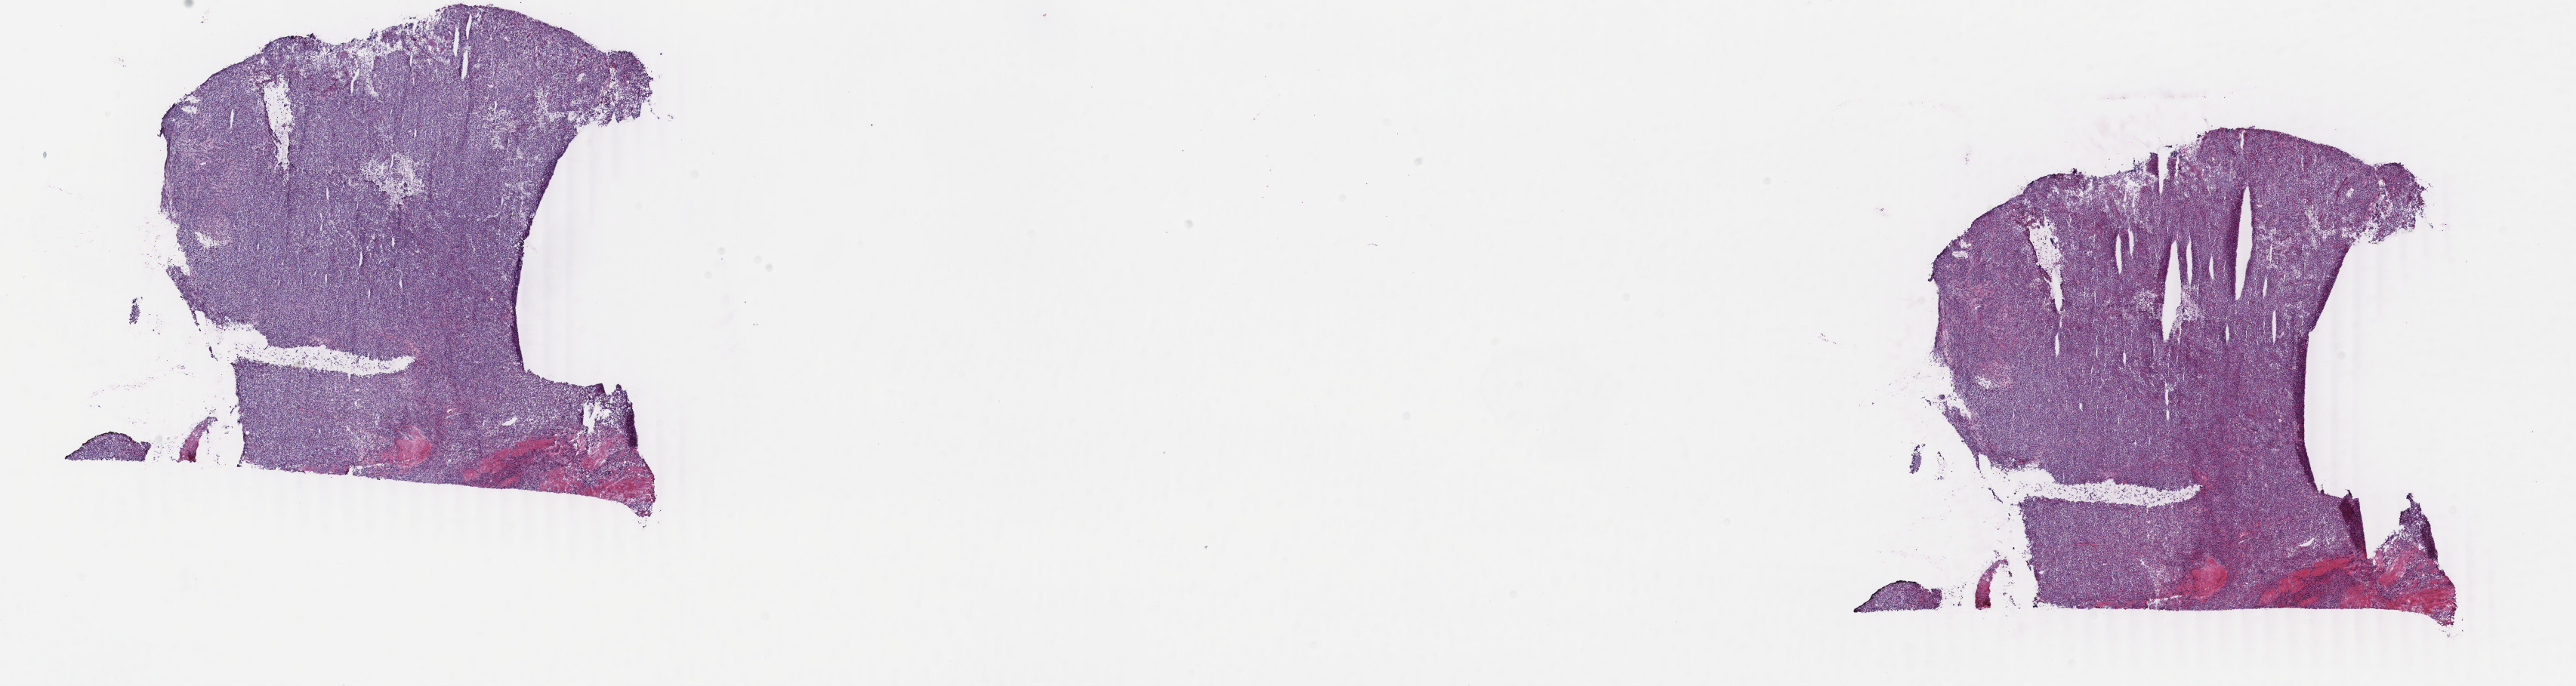
H&E-stained whole-slide image — whole scanned area (about 27.1 x 7.2 mm) shown as a low-resolution overview; frozen section; sample: primary tumour, bladder. Patient: female, age at initial diagnosis 57 years. Histologic grade: high grade. Composition of this section per pathologist review: tumour cells 90%, tumour nuclei 96%, normal cells 0%, stromal cells 5%, necrosis 5%. Inflammatory infiltration, as recorded: lymphocyte infiltration 2%, monocyte infiltration 0%, neutrophil infiltration 0%.
AJCC pathologic stage: III. Diagnosis: Transitional cell carcinoma.